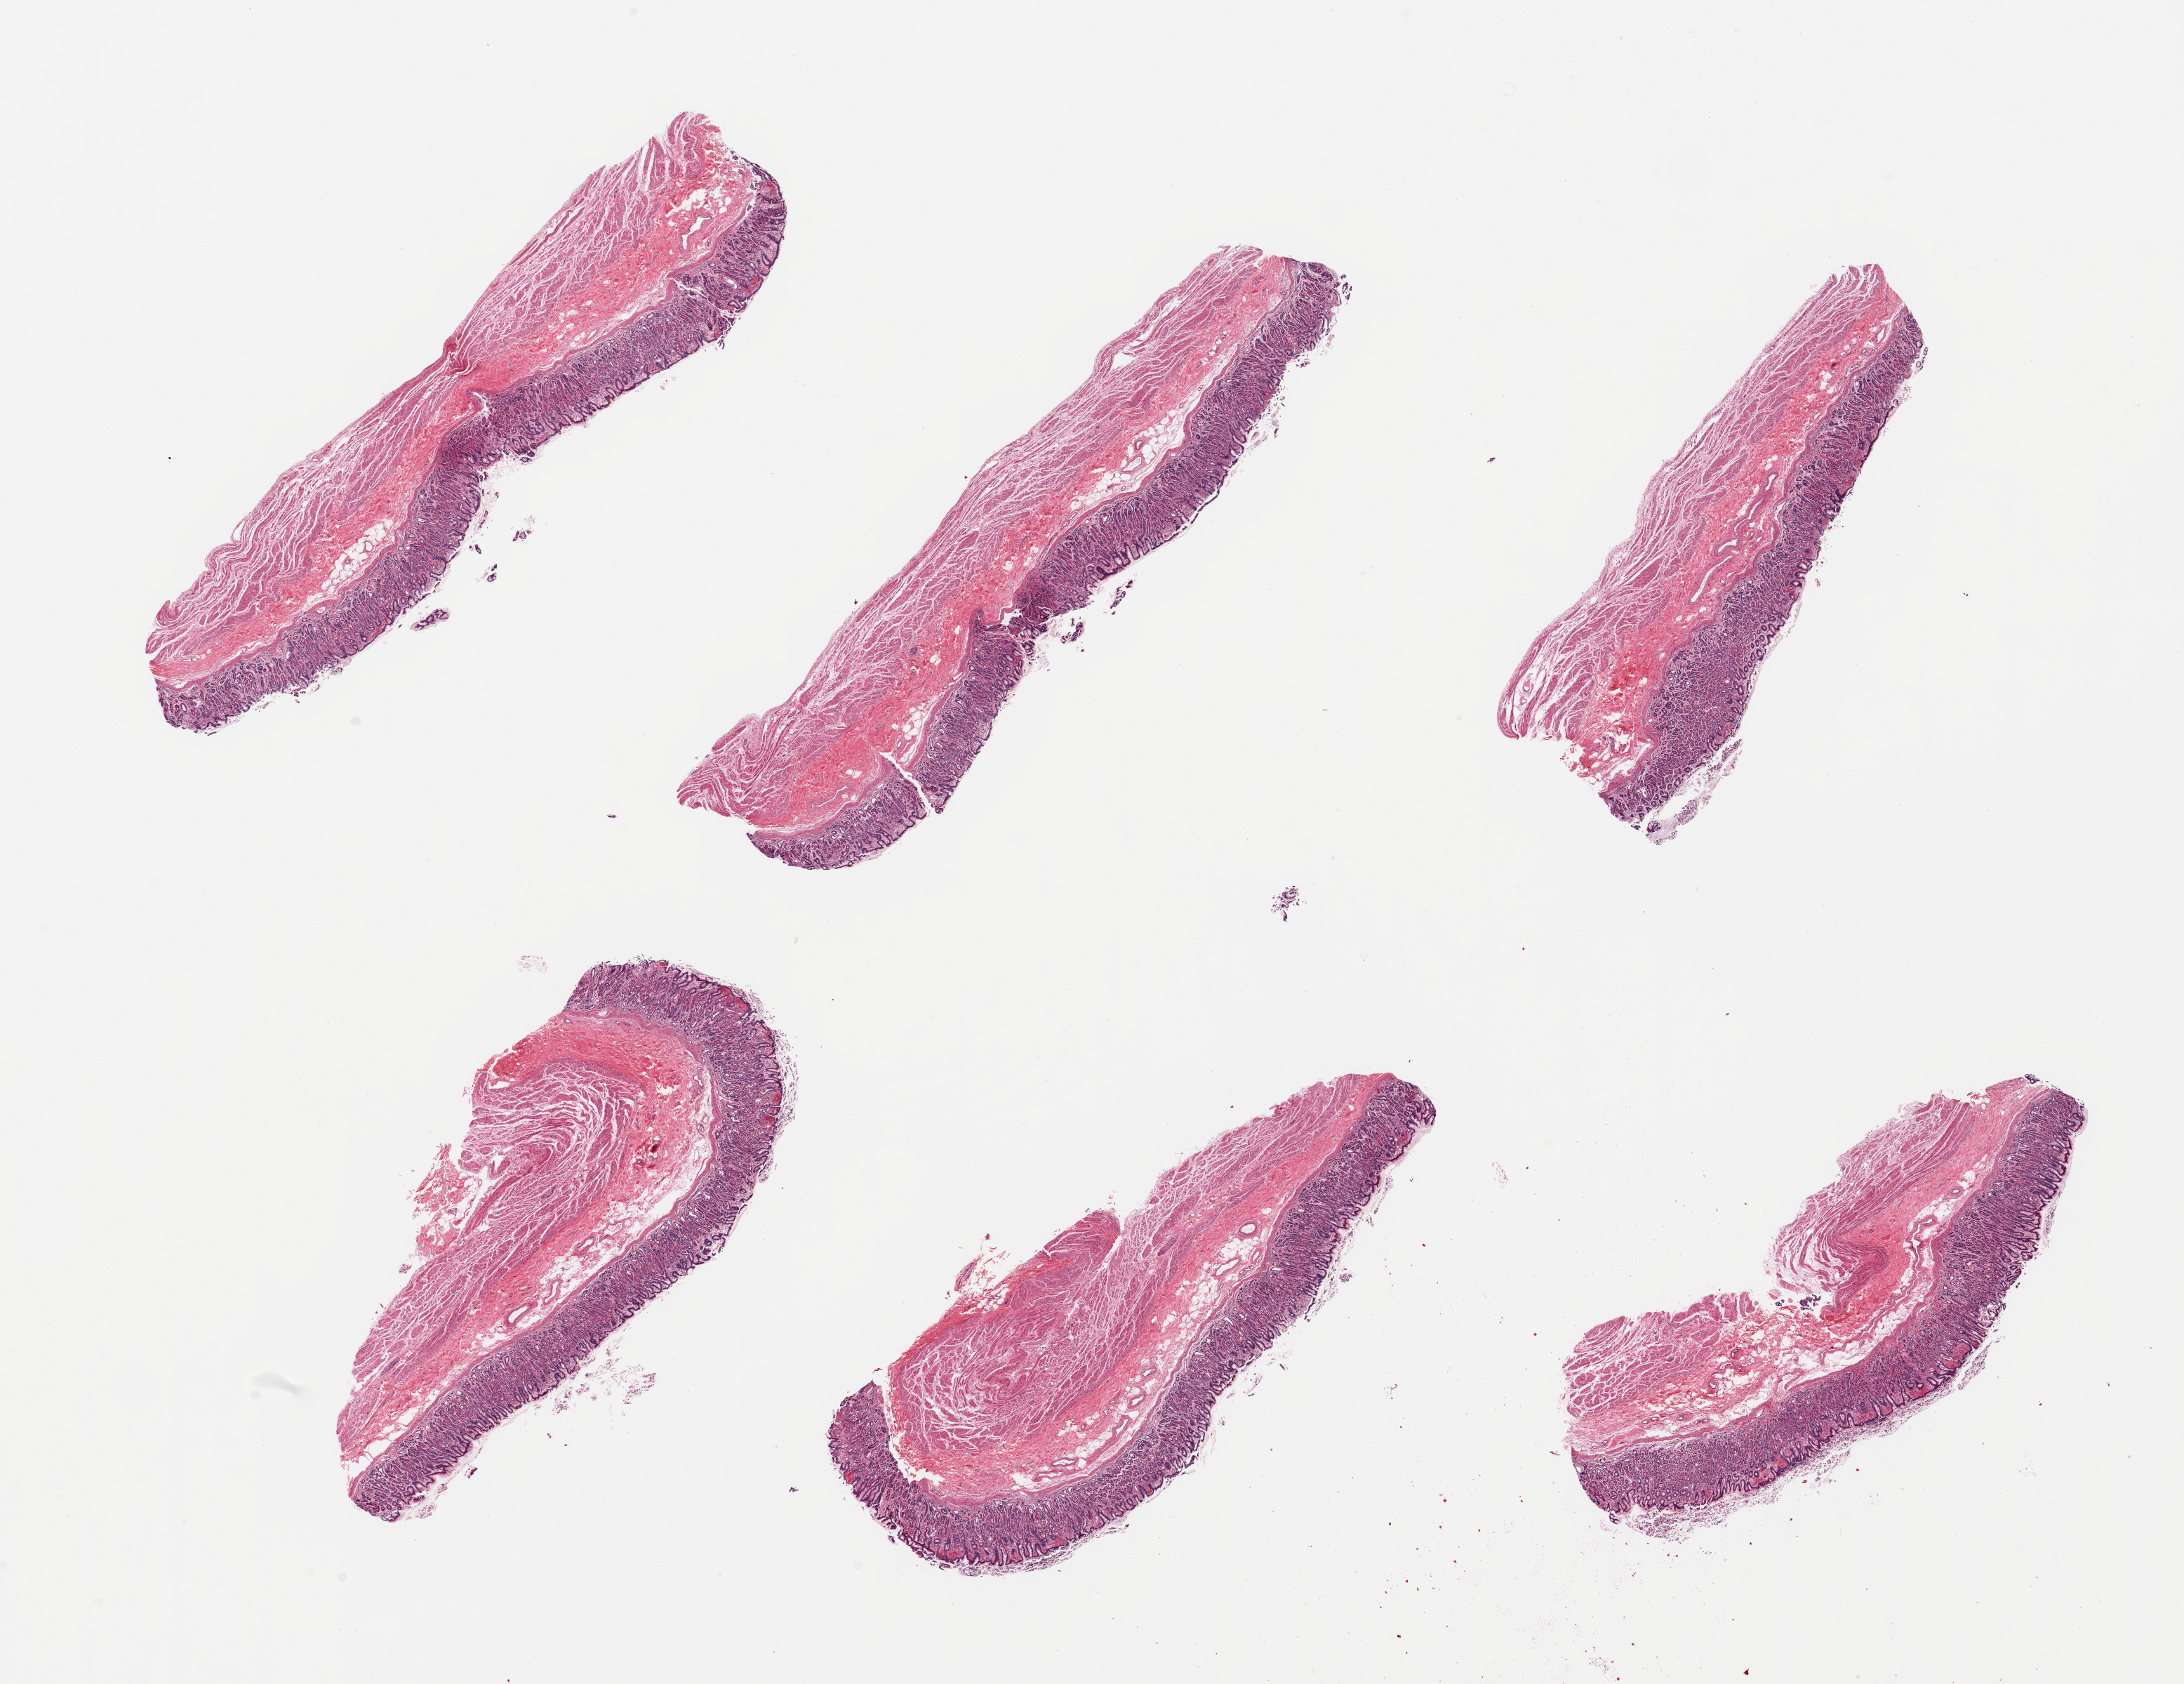
Digitized haematoxylin and eosin-stained section — whole scanned area (about 24.6 x 19.0 mm, slide scanned at 20x) shown as a low-resolution overview, PAXgene-fixed, paraffin-embedded tissue, sampled site (target tissue): stomach, donor tissue sample. Donor: female.
Review note (as recorded): 6 pieces; well dissected.